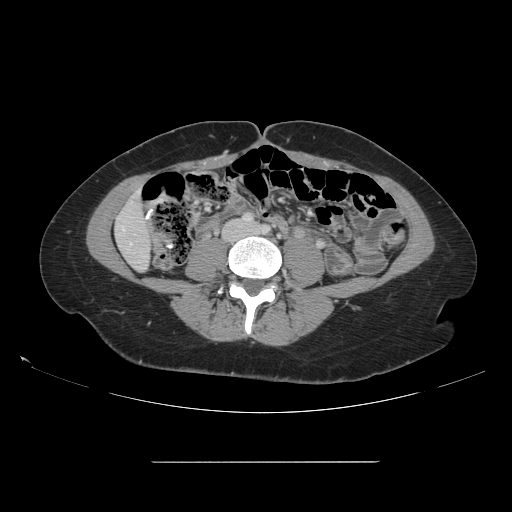
Contrast-enhanced abdominal CT, one axial slice. Slice 20 of 151 in the series (ordered by position). 120 kVp. Soft-tissue window (W 400 / L 40 HU). 512 × 512 image matrix, field of view 421 × 421 mm. Female patient, age 46 years. Case-level facts recorded for this patient, not image findings: diagnosis: colorectal cancer liver metastases, imaged before liver resection; multiple liver metastases: yes; largest metastasis: 3 cm; disease in both lobes: yes.
Annotated regions visible in this slice (expert manual segmentation):
- liver: bounding box [x1, y1, x2, y2] px = [117, 195, 151, 270]
- planned liver remnant (the part of the liver to remain after resection): [117, 195, 150, 270]